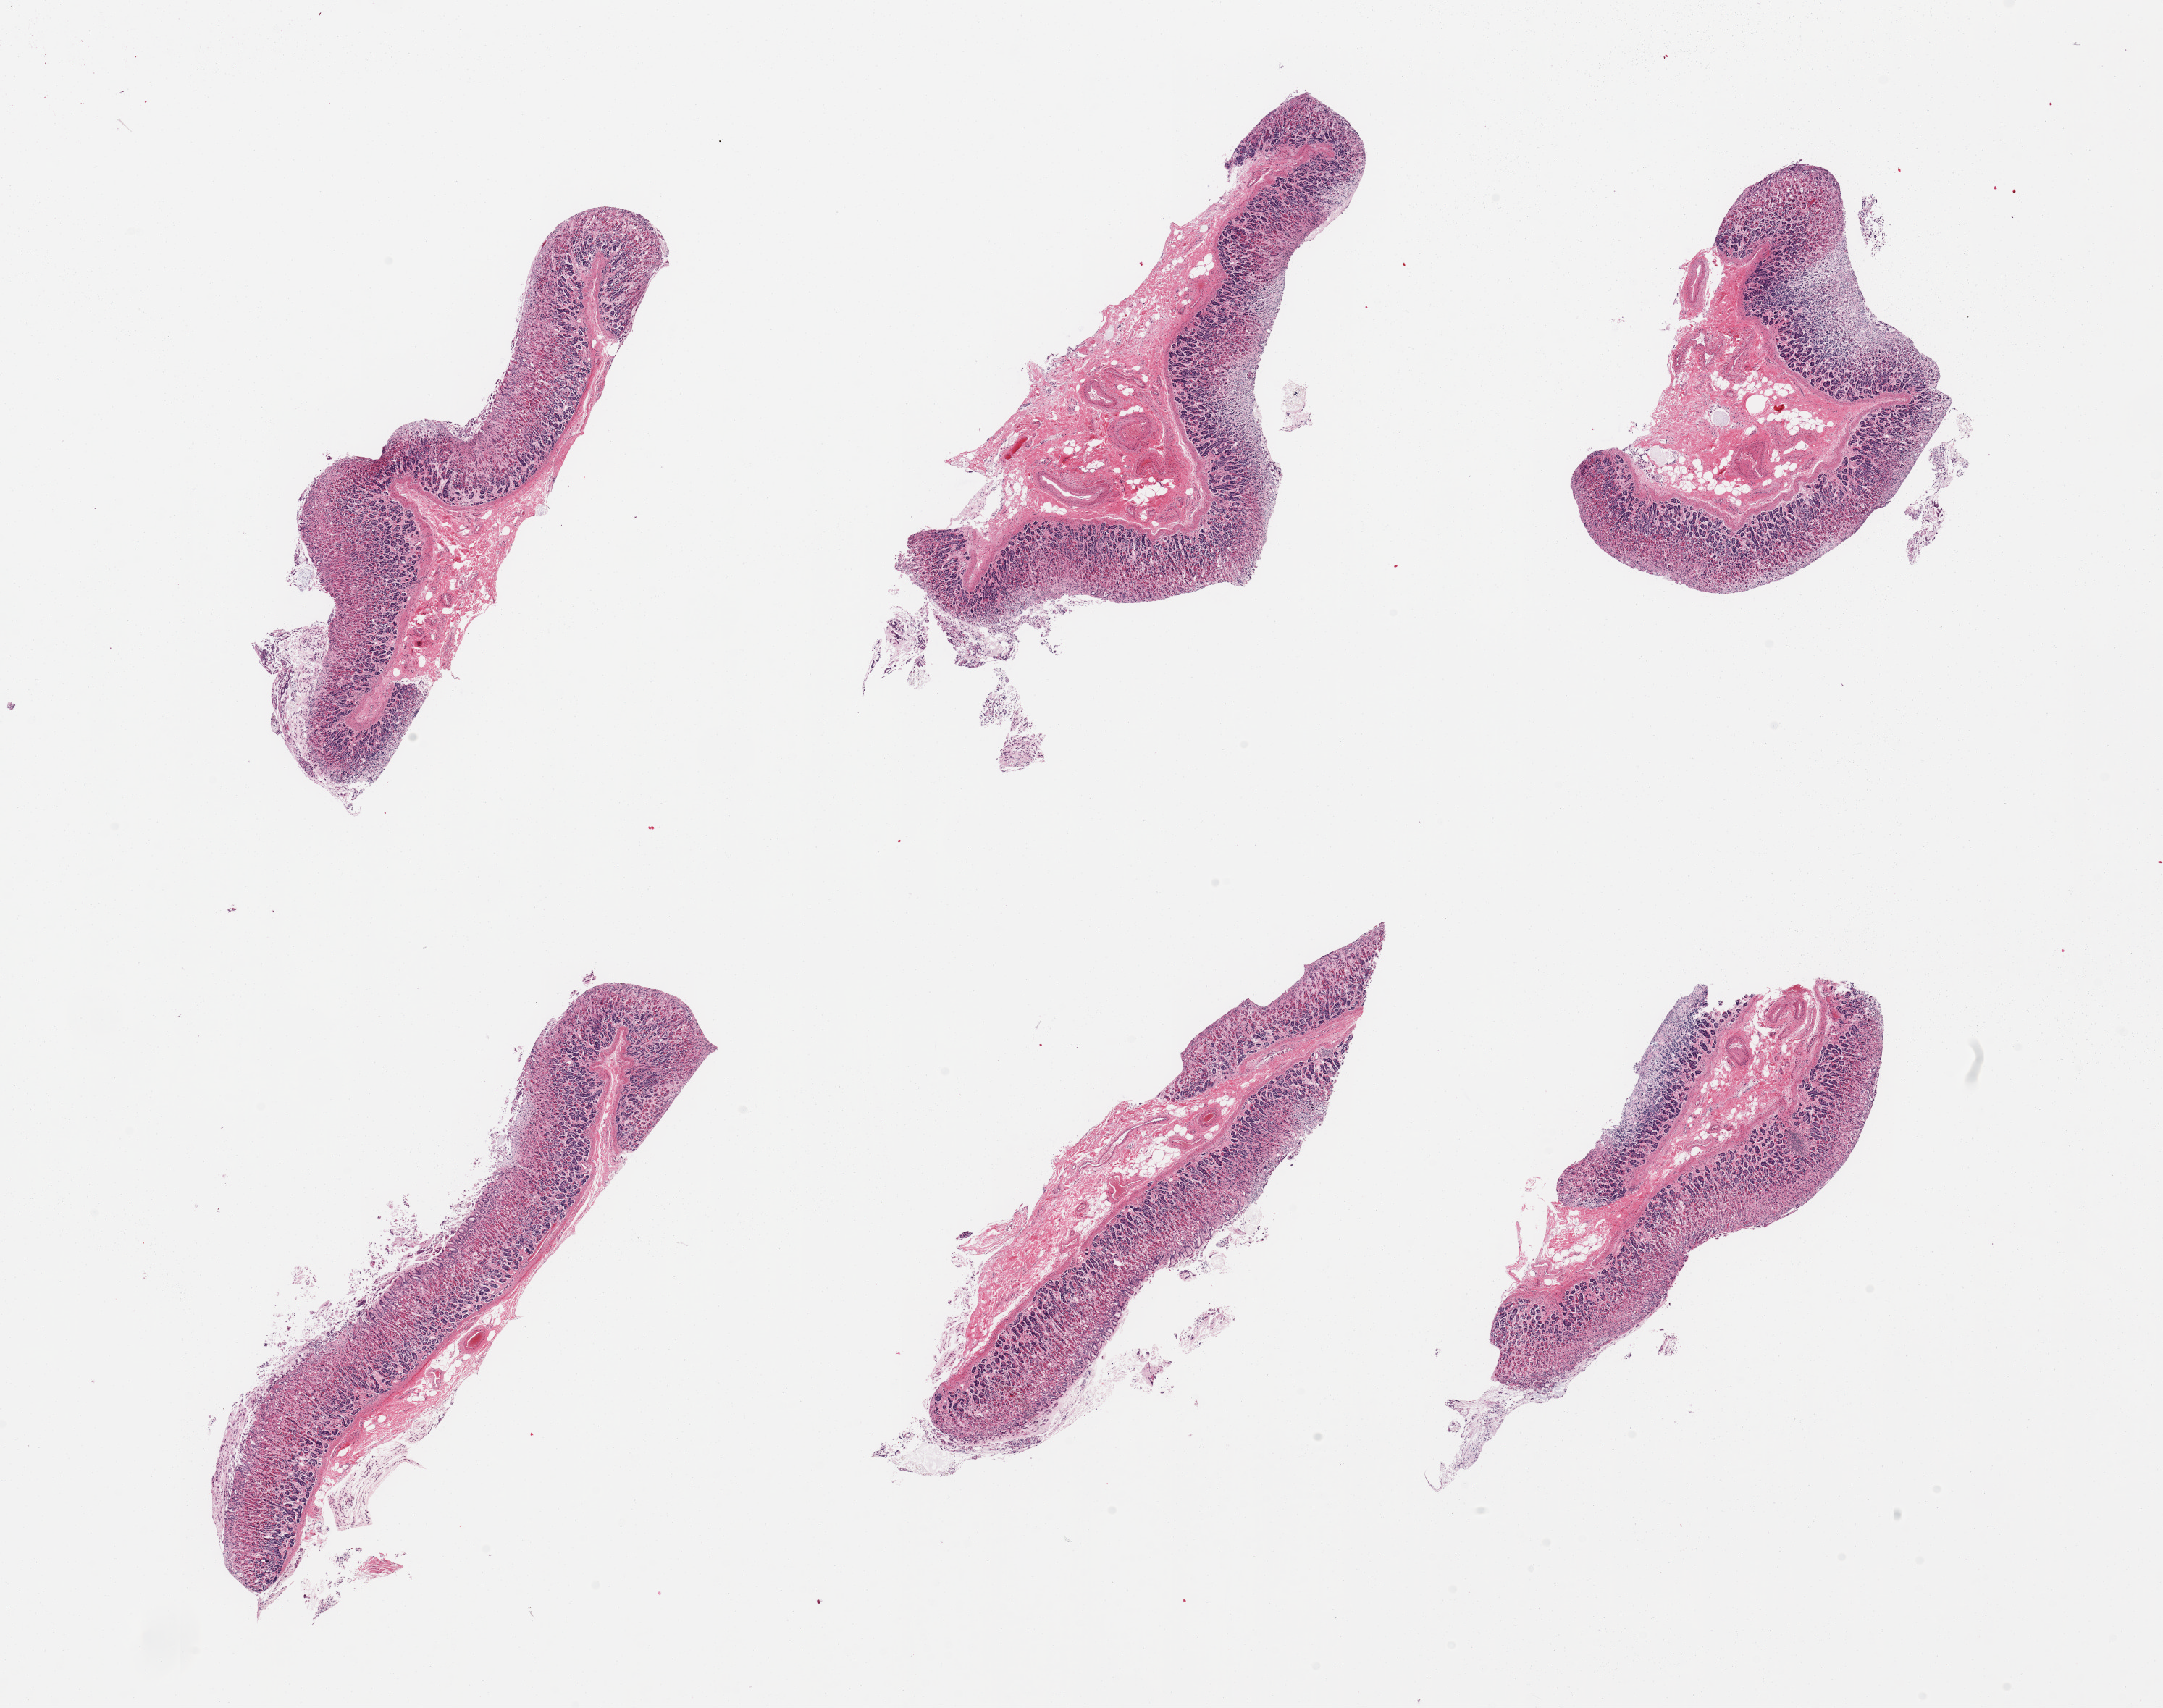
Haematoxylin and eosin whole-slide image — whole scanned area (about 23.6 x 18.7 mm, from a 20x scan) shown as a low-resolution overview. PAXgene-fixed paraffin-embedded (PFPE) section. Target tissue: stomach. Tissue donor sample. Donor: male.
Reviewer comment on this tissue sample: 6 pieces; partially autolyzed mucosa, submucosa (target is full thickness).